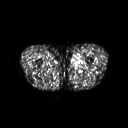
FDG PET of an extremity soft-tissue mass (from a PET/CT study), one axial slice; slice 252 of 311 in the series (ordered by position); 3.27 mm slice thickness; 128 × 128 image matrix, field of view 500 × 500 mm. Male patient, age 29 years. From the clinical record (not read from this slice): histological type: mixoid liposarcoma; grade: low; site of the primary tumour: left thigh.
Outlined on this slice (expert contour drawn on MRI and transferred to this co-registered scan by the dataset authors):
- gross tumour volume (mass): bounding box [x1, y1, x2, y2] px = [70, 54, 82, 66]